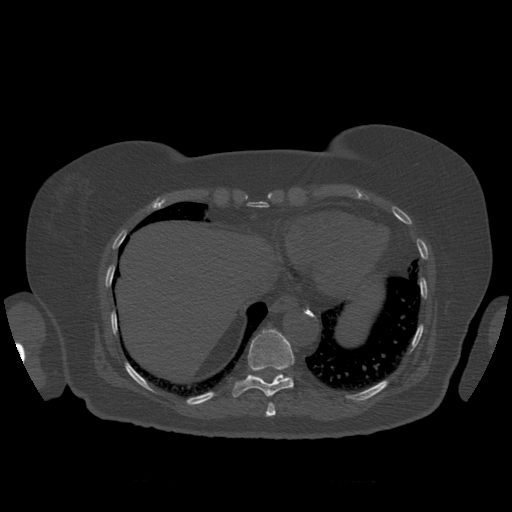
CT including the spine, one axial slice. Slice 340 of 399 in the series (ordered by position). Reconstruction kernel STANDARD. Bone window (W 1800 / L 400 HU). 512 × 512 image matrix, field of view 404 × 404 mm. Patient age 81 years. Case-level facts recorded for this patient, not image findings: primary cancer: renal; vertebrae with lytic lesions (as recorded): L1.
Outlined on this slice (semi-automatic segmentation, software-assisted and operator-edited):
- T10 vertebra: bounding box (x1, y1, x2, y2) in pixels: (233, 330, 295, 398)
- T9 vertebra: (266, 403, 276, 417)